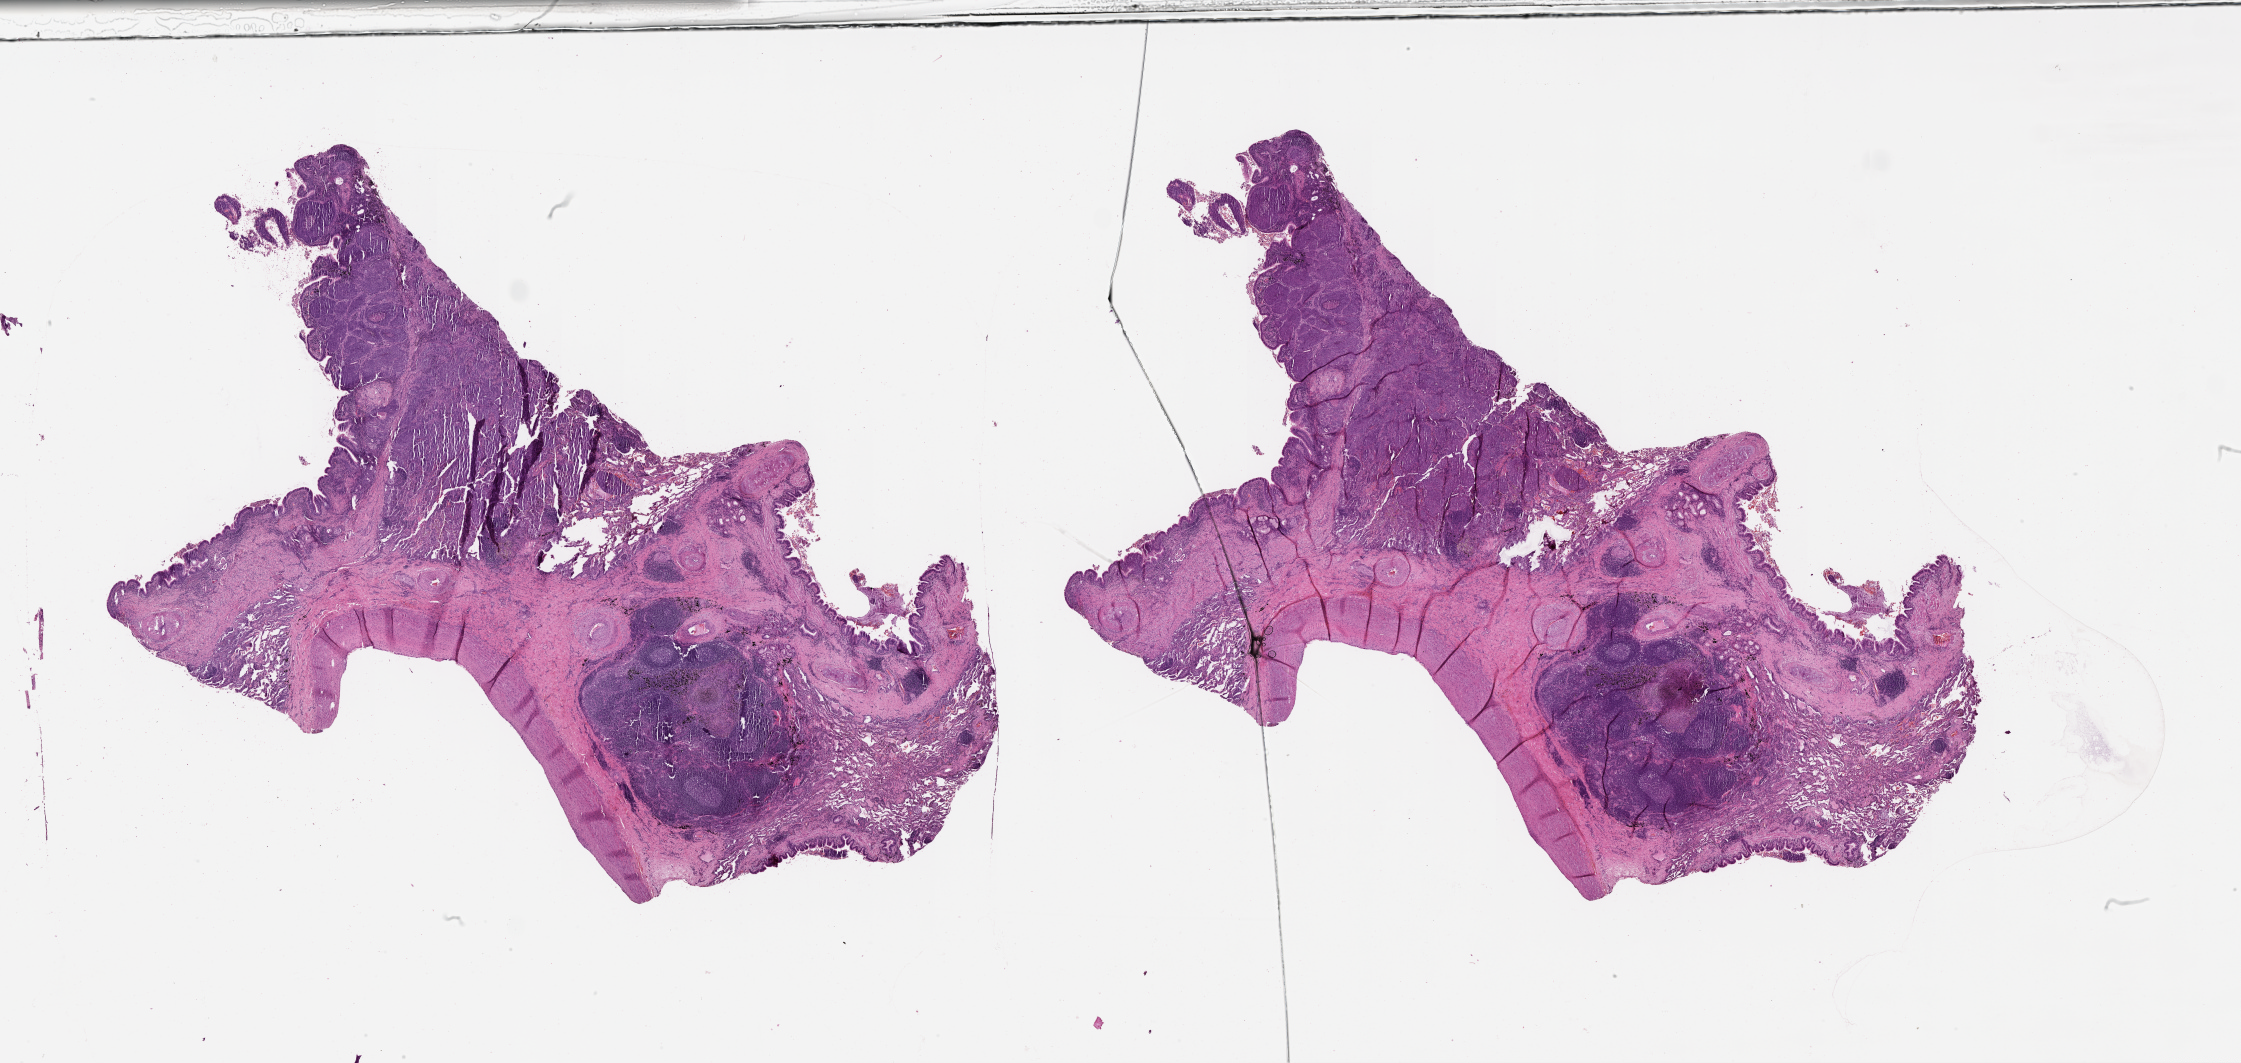
Whole-slide histology image, H&E-stained — whole scanned area (about 36.1 x 17.1 mm, slide scanned at 20x) shown as a low-resolution overview; lung, tumour tissue. Patient: male, age 59 years.
Patient diagnosis (cohort enrolment): squamous cell carcinoma (lung).